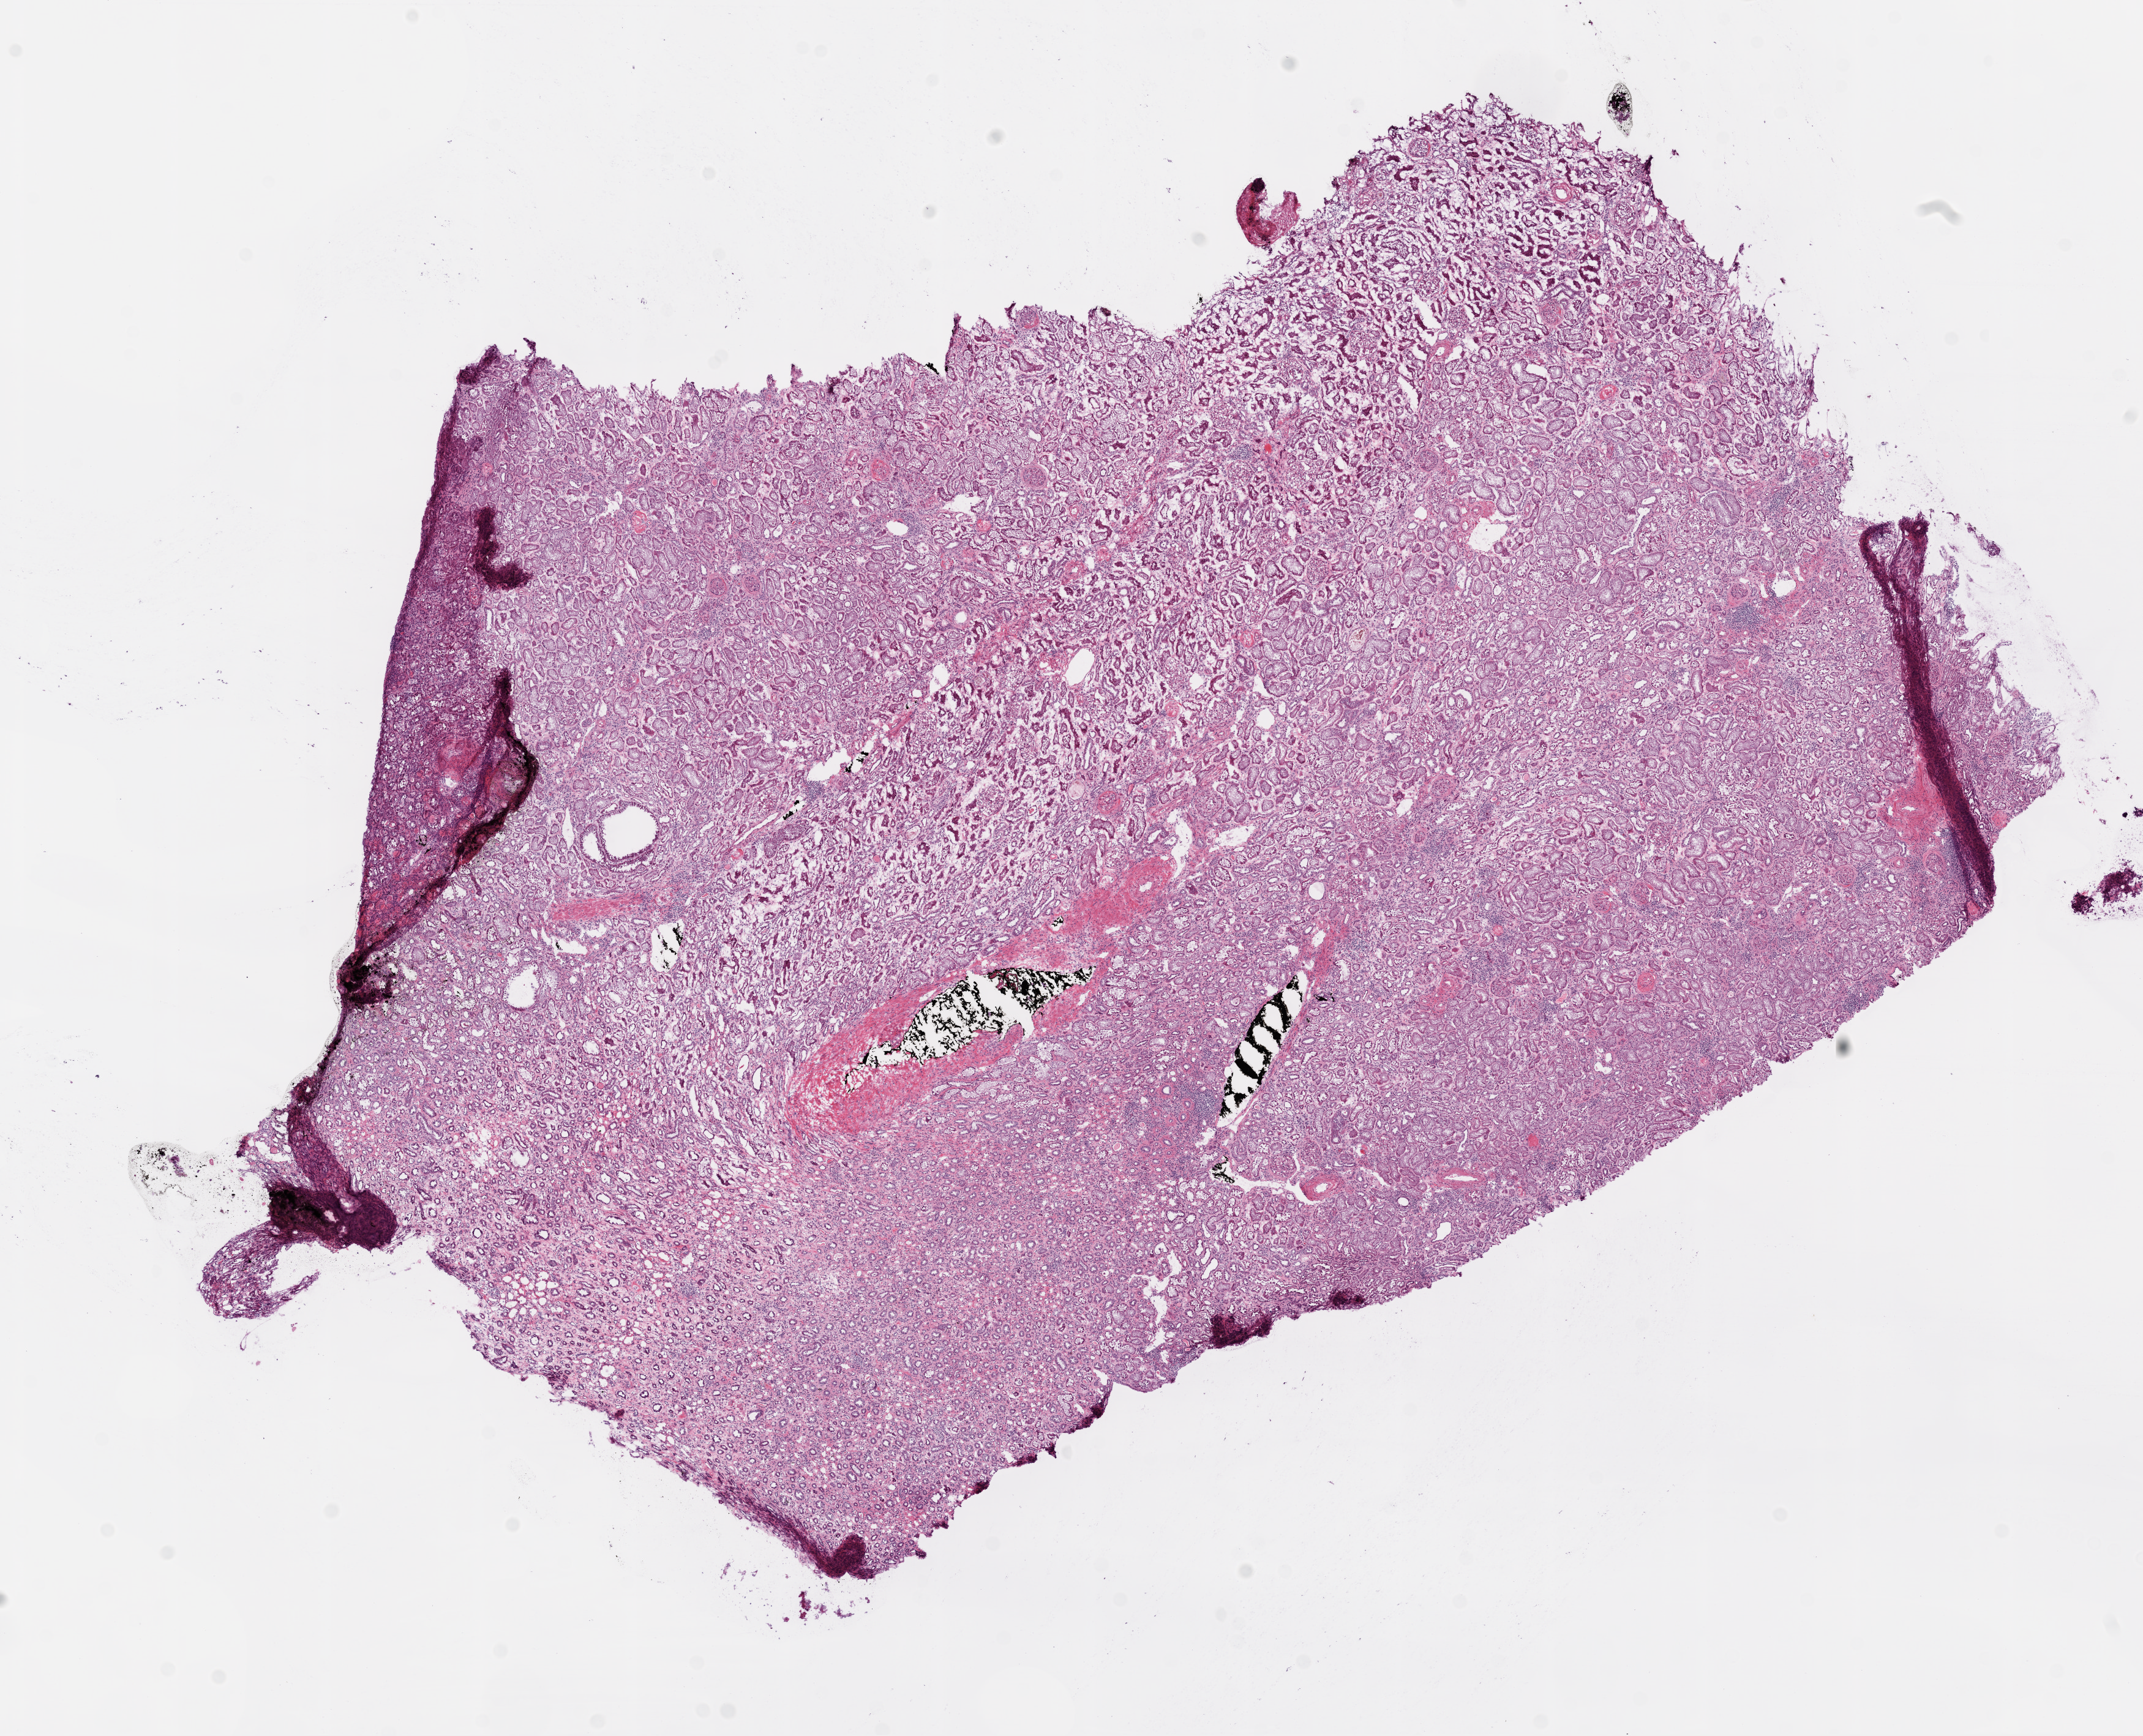
Whole-slide histology image, H&E, a low-resolution overview of the entire scanned area, about 14.0 x 11.4 mm. Frozen section from the top of the tissue portion. Solid tissue normal (non-tumour tissue) sample from the kidney. Male patient; age at initial diagnosis 59 years.
• this section: solid tissue normal sample (biorepository sample class)
• patient diagnosis: Clear cell adenocarcinoma, NOS